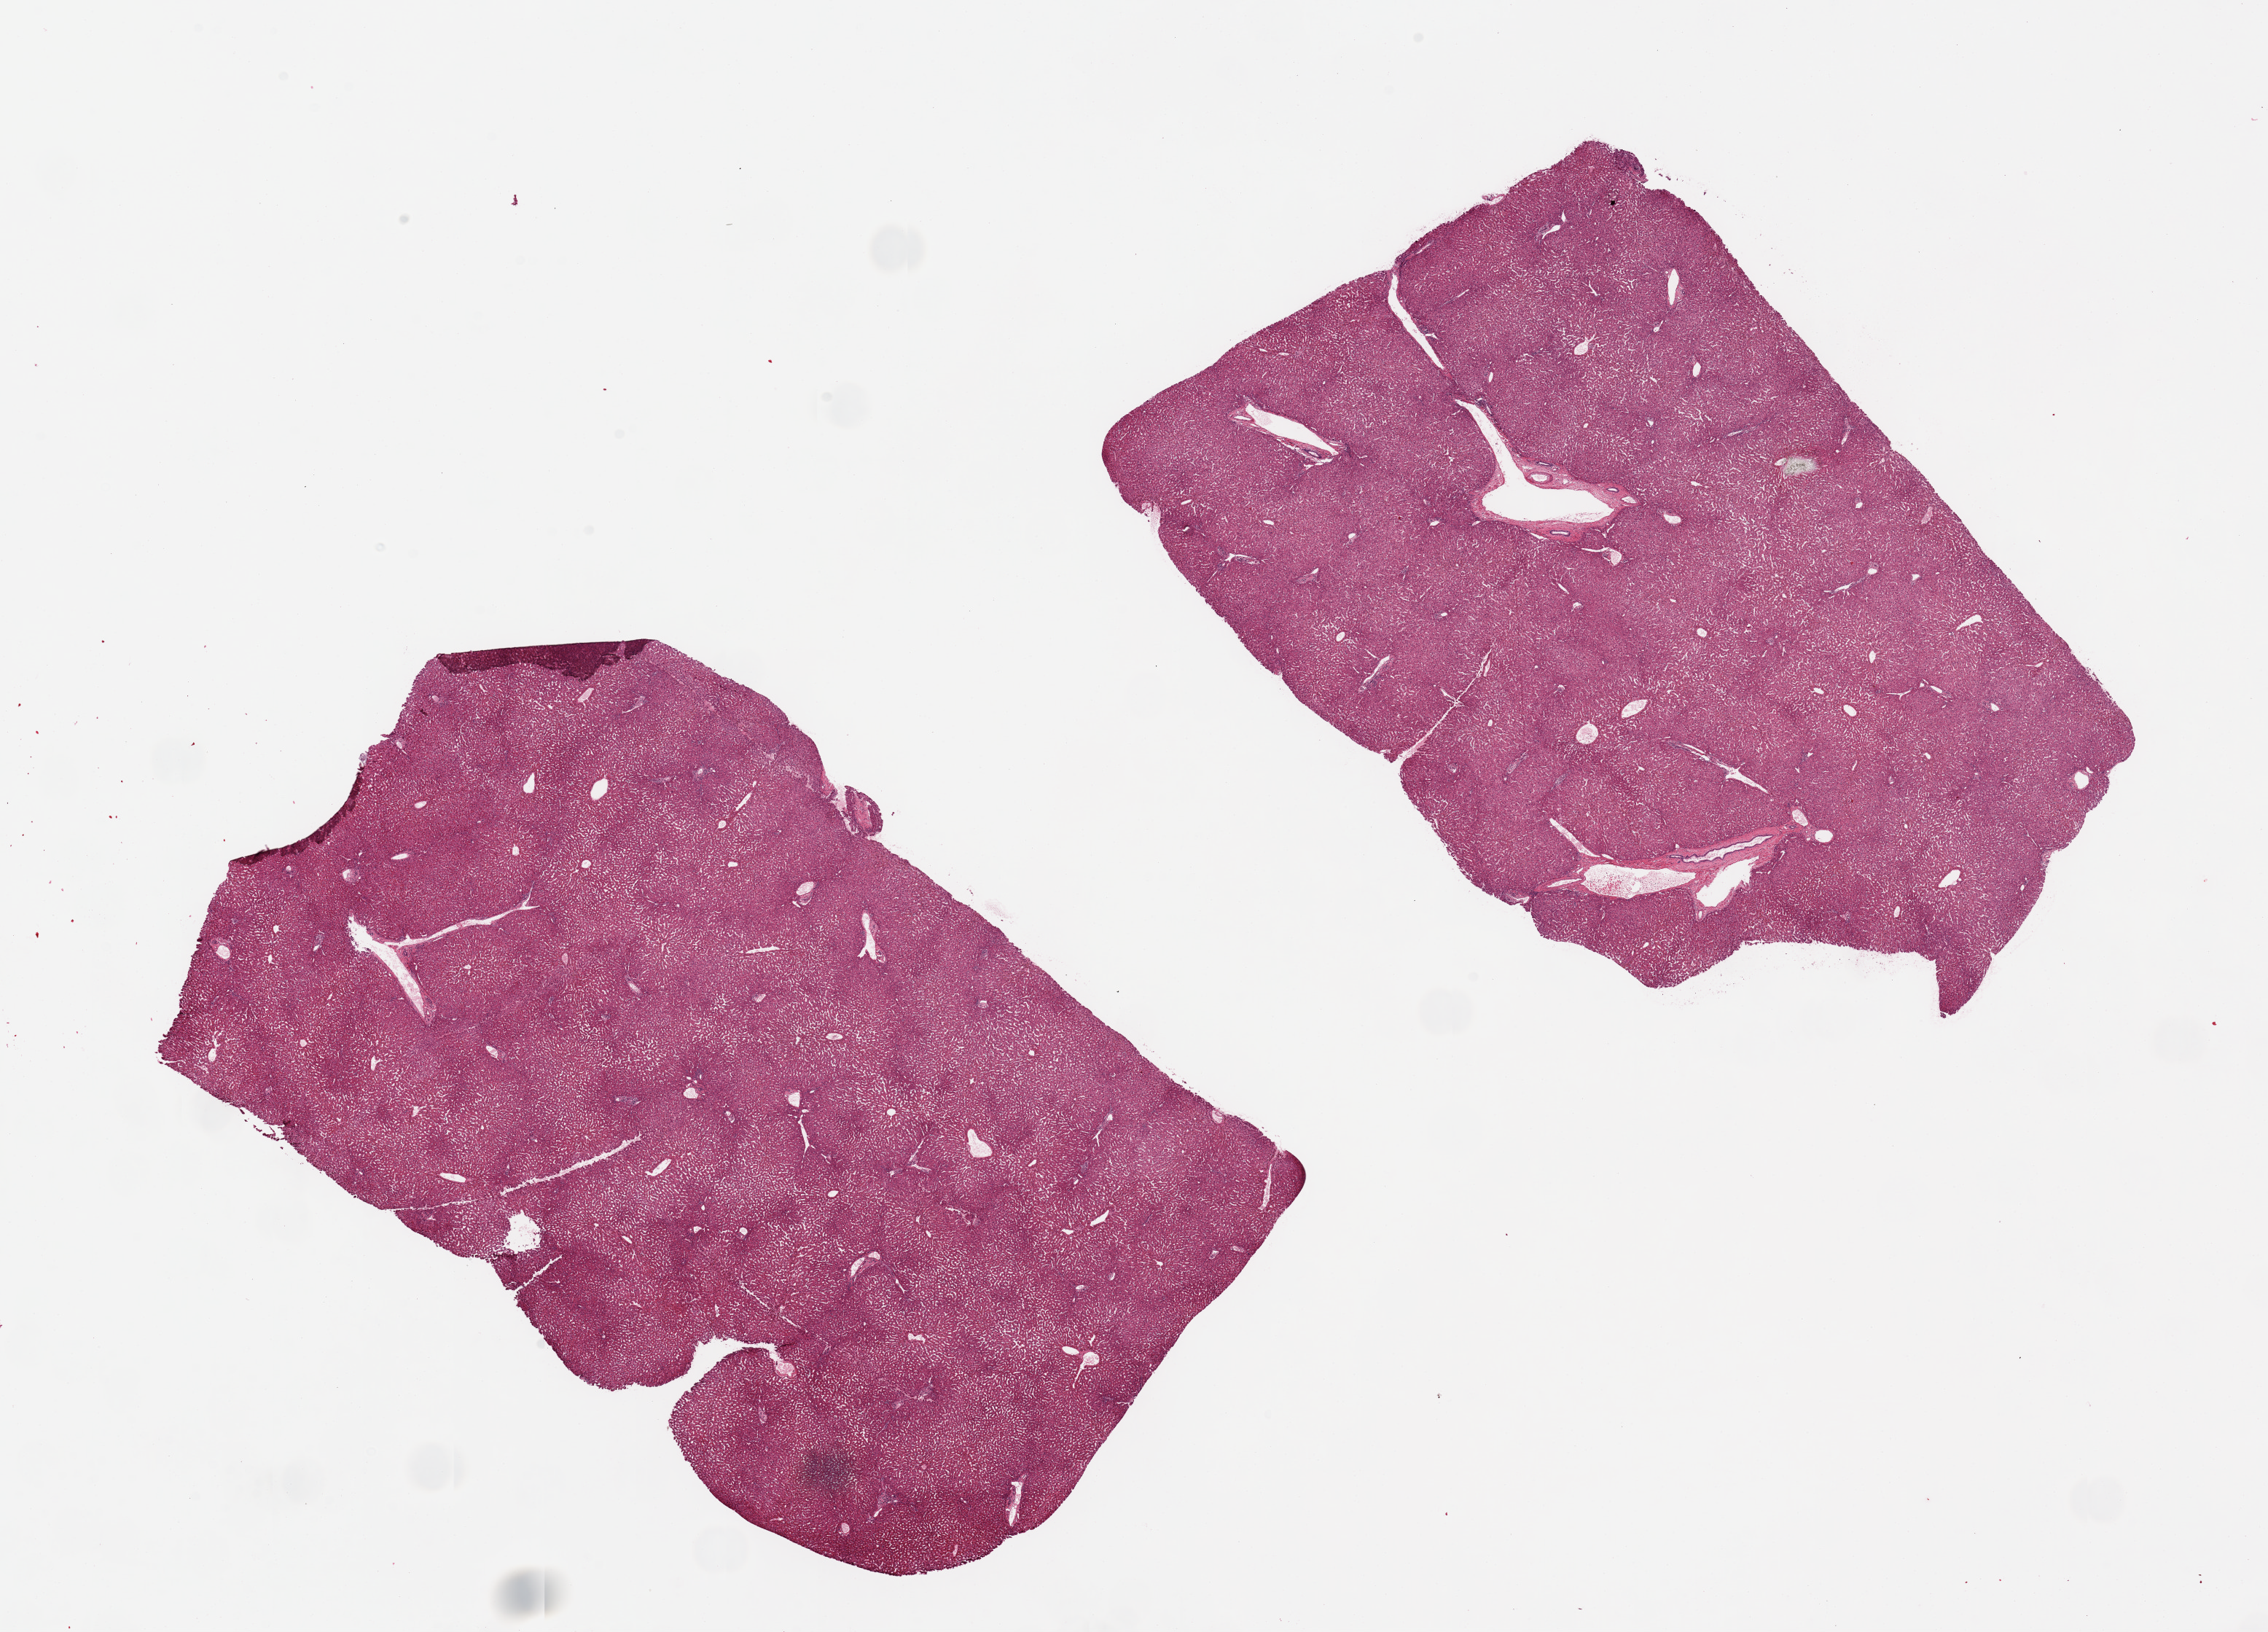
Haematoxylin and eosin whole-slide image, shown as a low-resolution overview of the whole scanned area (about 24.6 x 17.7 mm), PAXgene-fixed paraffin-embedded (PFPE) section, sampled site (target tissue): liver, tissue donor sample. Female donor.
Reviewer comment on this tissue sample: 2 pieces.